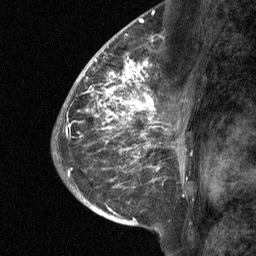
Breast MRI (dynamic contrast-enhanced), one sagittal slice. Position 37 of 64 along the scan axis. Dynamic contrast-enhanced study with each time point stored as its own series, time point 2 of 3 at this slice position (early post-contrast, ordered by acquisition time). 1.5 T. TE 4.8 ms, TR 27 ms. 256 × 256 image matrix, field of view 180 × 180 mm. Patient: female, 59 years. From the clinical record (not read from this slice): setting: breast cancer imaged before/during neoadjuvant chemotherapy; receptor status: triple-negative.
Outlined on this slice (semi-automatically segmented with operator editing):
- analysis volume of interest (the breast-tissue region the enhancement analysis was run in; not a lesion): bounding box <122,58,174,109> (left, top, right, bottom; pixels)
- tumour enhancement mask (voxels above the 90 % enhancement threshold inside the analysis volume of interest): <122,58,156,109>